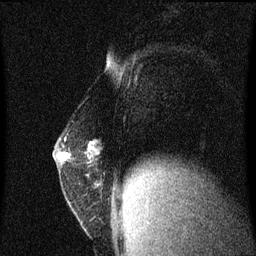
Breast MRI (dynamic contrast-enhanced), one sagittal slice. Slice 24 of 60 in the series (ordered by position). Dynamic contrast-enhanced series, image 2 of 3 at this slice position (ordered by acquisition). 1.5 T. TE 4.2 ms, TR 8.4 ms. 2 mm slice thickness. 256 × 256 image matrix, field of view 200 × 200 mm. Patient: female, 52 years. Case-level facts recorded for this patient, not image findings: setting: breast cancer imaged before/during neoadjuvant chemotherapy; receptor status: HER2-positive.
Annotated regions visible in this slice (semi-automatic segmentation, software-assisted and operator-edited):
- analysis volume of interest (the breast-tissue region the enhancement analysis was run in; not a lesion): bounding box [x1, y1, x2, y2] px = [54, 128, 119, 191]
- tumour enhancement mask (voxels above the 70 % enhancement threshold inside the analysis volume of interest): [89, 144, 91, 149]